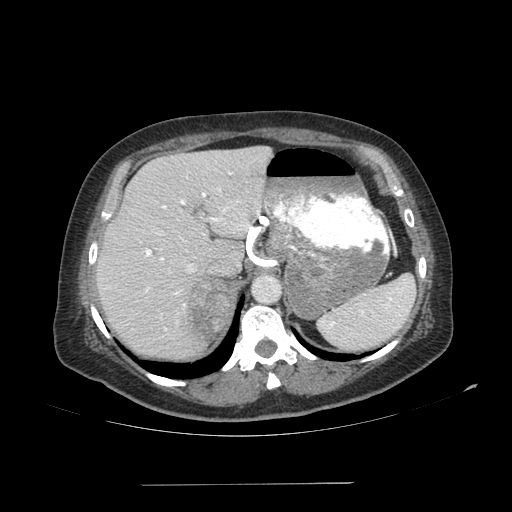
Contrast-enhanced abdominal CT, one axial slice. Slice 78 of 113 in the series (ordered by position). Reconstruction kernel SOFT. Soft-tissue window (W 400 / L 40 HU). 2.5 mm slice thickness. 512 × 512 image matrix, field of view 440 × 440 mm. Patient: female, 67 years. From the clinical record (not read from this slice): diagnosis: adrenocortical carcinoma; tumour side: right adrenal; tumour size at pathology: 9.8 cm; Ki-67 index: 59 %; stage (as recorded): 4.
Annotated regions visible in this slice (semi-automatic segmentation, software-assisted and operator-edited):
- mass: box from (x=187, y=278) to (x=229, y=336) px